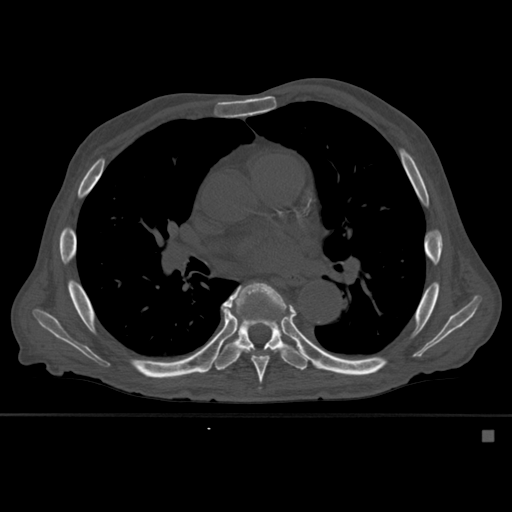
CT including the spine, one axial slice. Bone window (W 1800 / L 400 HU). 1.5 mm slice thickness. 512 × 512 image matrix, field of view 373 × 373 mm. Male patient, age 78 years. From the clinical record (not read from this slice): primary cancer: prostate.
Outlined on this slice (semi-automatically segmented with operator editing):
- T7 vertebra: bounding box (x1, y1, x2, y2) in pixels: (224, 282, 296, 391)
- T8 vertebra: (212, 283, 309, 371)